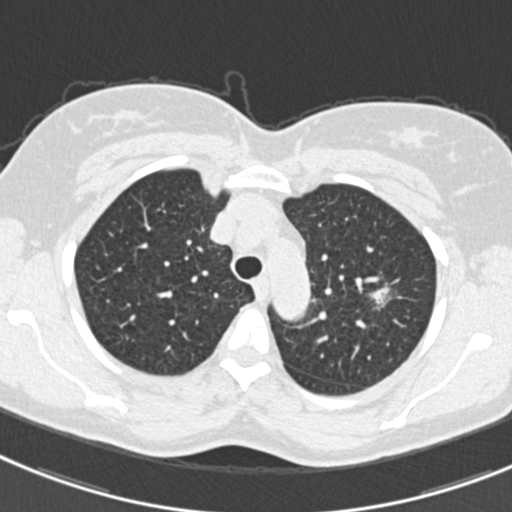
Low-dose screening chest CT, one axial slice; slice 245 of 309 in the series (ordered by position); 120 kVp; lung window (W 1500 / L -600 HU); 1 mm slice thickness; 512 × 512 image matrix.
Outlined on this slice (manually delineated by an expert):
- lesion 1 (tumor, upper lobe of left lung): bounding box (x1, y1, x2, y2) in pixels: (371, 287, 389, 304)